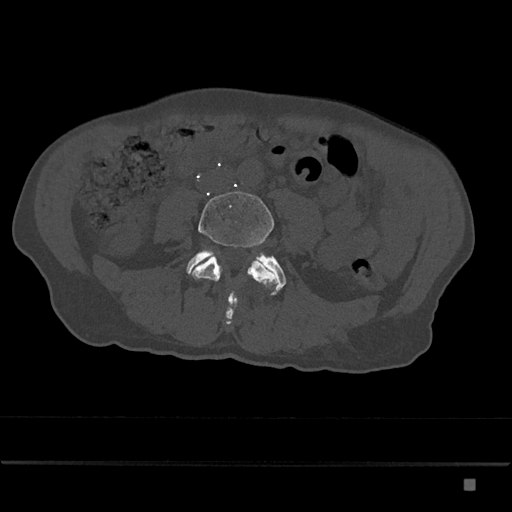
CT including the spine, one axial slice. Bone window (W 1800 / L 400 HU). 0.5 mm slice thickness. 512 × 512 image matrix, field of view 390 × 390 mm. Male patient, age 72 years. From the clinical record (not read from this slice): primary cancer: prostate.
Outlined on this slice (semi-automatically segmented with operator editing):
- L4 vertebra: bounding box (x1, y1, x2, y2) in pixels: (190, 191, 278, 307)
- L5 vertebra: (186, 249, 286, 324)